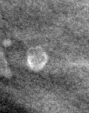
Cropped region of a digitized screen-film mammogram centred on a radiologist-marked abnormality, right breast, CC view, BI-RADS breast density category 3 (scale 1–4).
Calcifications, morphology round and regular / lucent centered; BI-RADS assessment category 2; benign without callback (not worked up further).